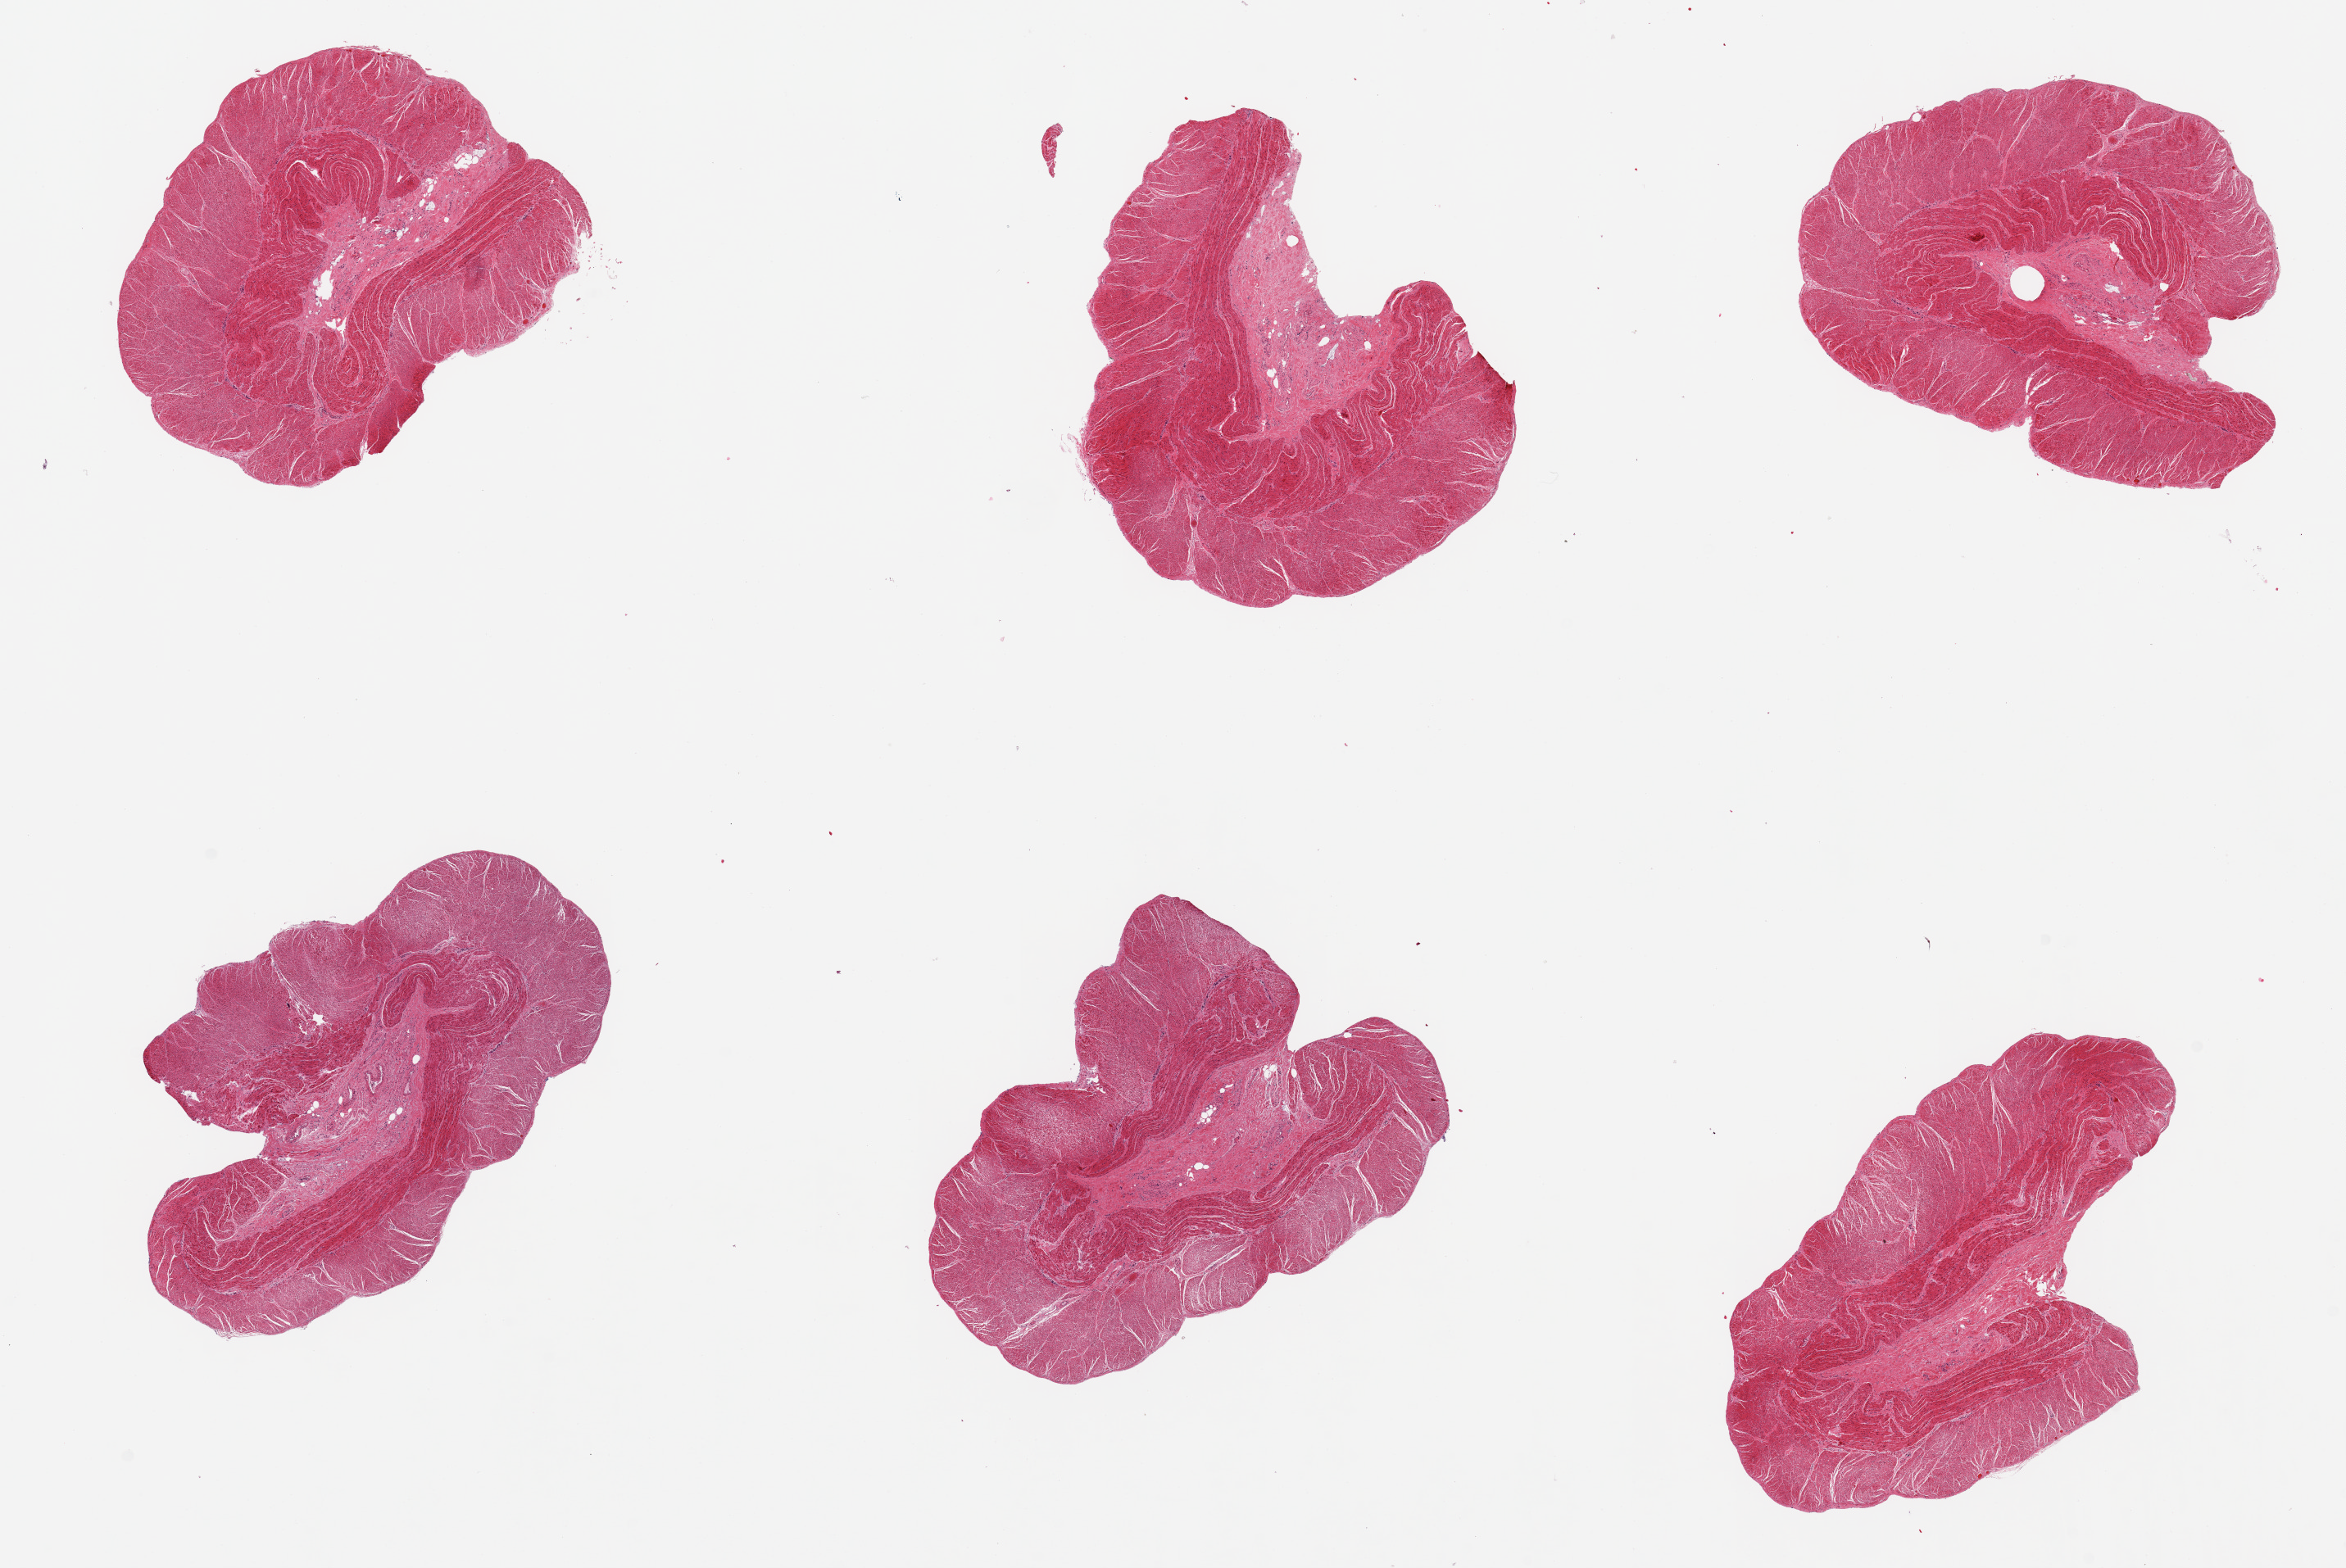
Digitized haematoxylin and eosin-stained section, low-resolution overview of the scanned area, about 22.6 x 15.1 mm; PAXgene-fixed paraffin-embedded (PFPE) section; sampled site (target tissue): sigmoid colon; donor tissue sample. Donor: female.
• review note (as recorded): 6 pieces; well trimmed muscle and adjacent stroma